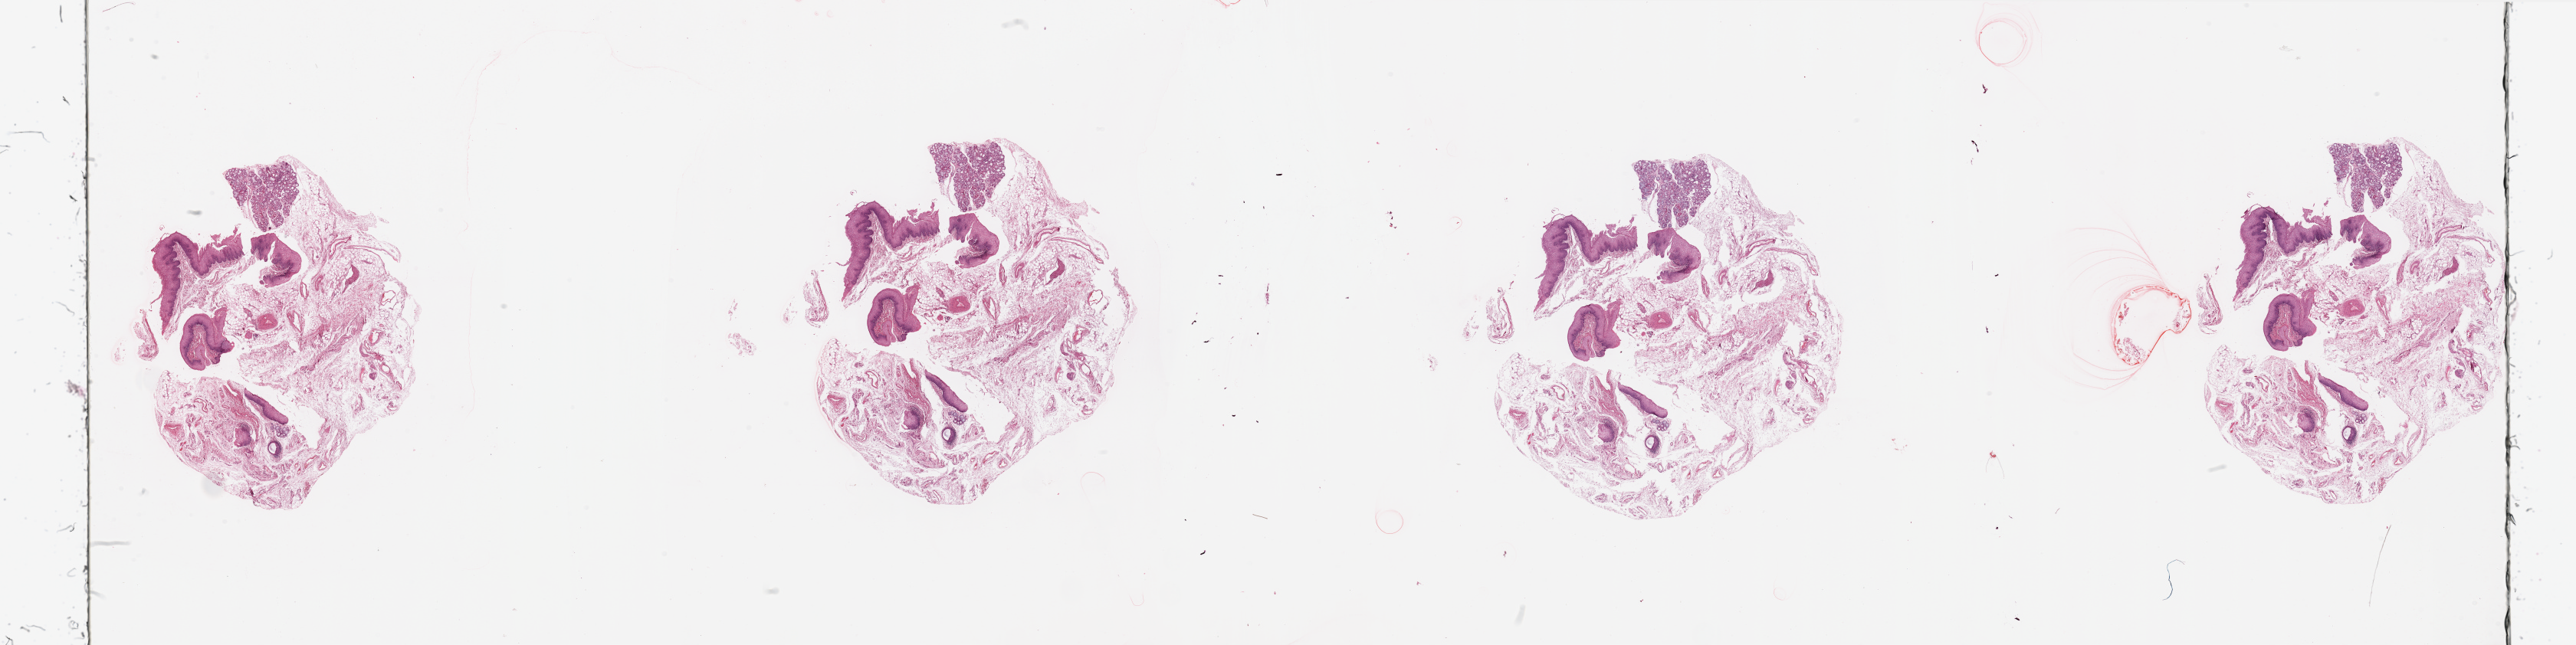
Whole-slide histology image, H&E-stained — a low-resolution overview of the entire scanned area, about 53.2 x 13.3 mm (from a 20x scan), head and neck, tissue type not recorded. Patient: male, age 68 years.
Patient diagnosis: Squamous cell carcinoma, NOS.